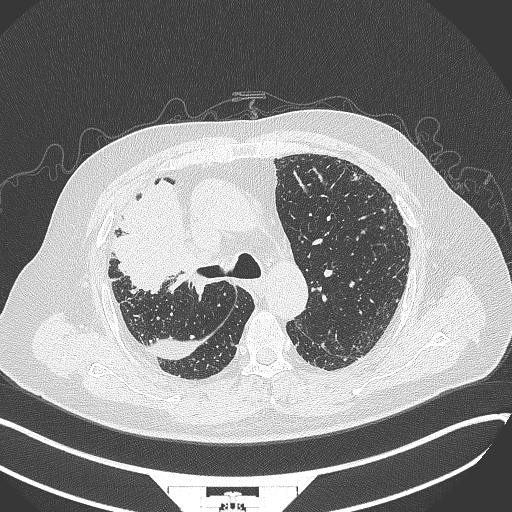
Chest CT, one axial slice. Slice 243 of 384 in the series (ordered by position). 120 kVp. Lung window (W 1500 / L -600 HU). 1 mm slice thickness. 512 × 512 image matrix, field of view 400 × 400 mm. Male patient, age 69 years. From the clinical record (not read from this slice): clinical TNM (as recorded): T4 N3 M1.
Outlined on this slice (bounding box drawn by a radiologist):
- lung tumour (recorded histology: adenocarcinoma): bounding box (x1, y1, x2, y2) in pixels: (96, 175, 192, 300)